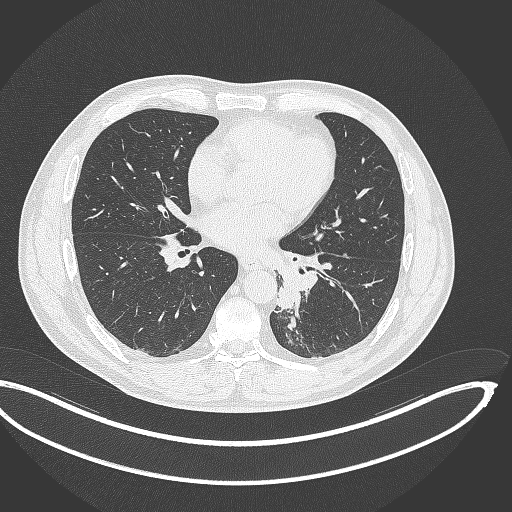
Chest CT, one axial slice; reconstruction kernel B70f; 120 kVp; lung window (W 1500 / L -600 HU); 1 mm slice thickness; 512 × 512 image matrix, field of view 442 × 442 mm. Male patient, age 50 years. From the clinical record (not read from this slice): clinical TNM (as recorded): T2a N3 M0.
Annotated regions visible in this slice (rectangle marked by the reading radiologist):
- lung tumour (recorded histology: squamous cell carcinoma): box from (x=275, y=279) to (x=304, y=312) px